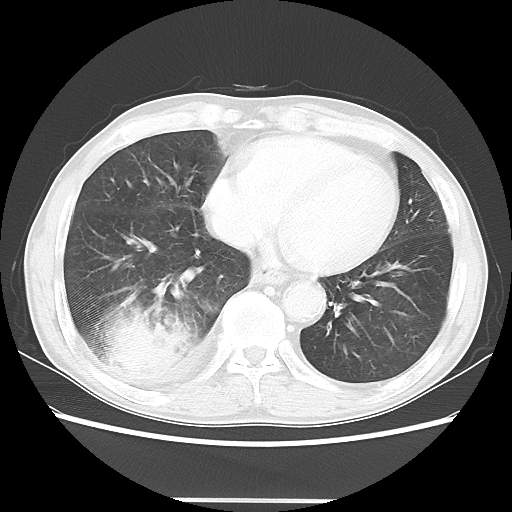
Chest CT, one axial slice; slice 13 of 48 in the series (ordered by position); reconstruction kernel LUNG; 100 kVp; lung window (W 1500 / L -600 HU); 5 mm slice thickness; 512 × 512 image matrix, field of view 361 × 361 mm. Patient: male, 66 years. Case-level facts recorded for this patient, not image findings: clinical TNM (as recorded): T4 N1 M1; histopathological grade: G3.
Structures marked on this image (bounding box drawn by a radiologist):
- lung tumour (recorded histology: small cell carcinoma): bounding box (x1, y1, x2, y2) in pixels: (87, 291, 200, 406)